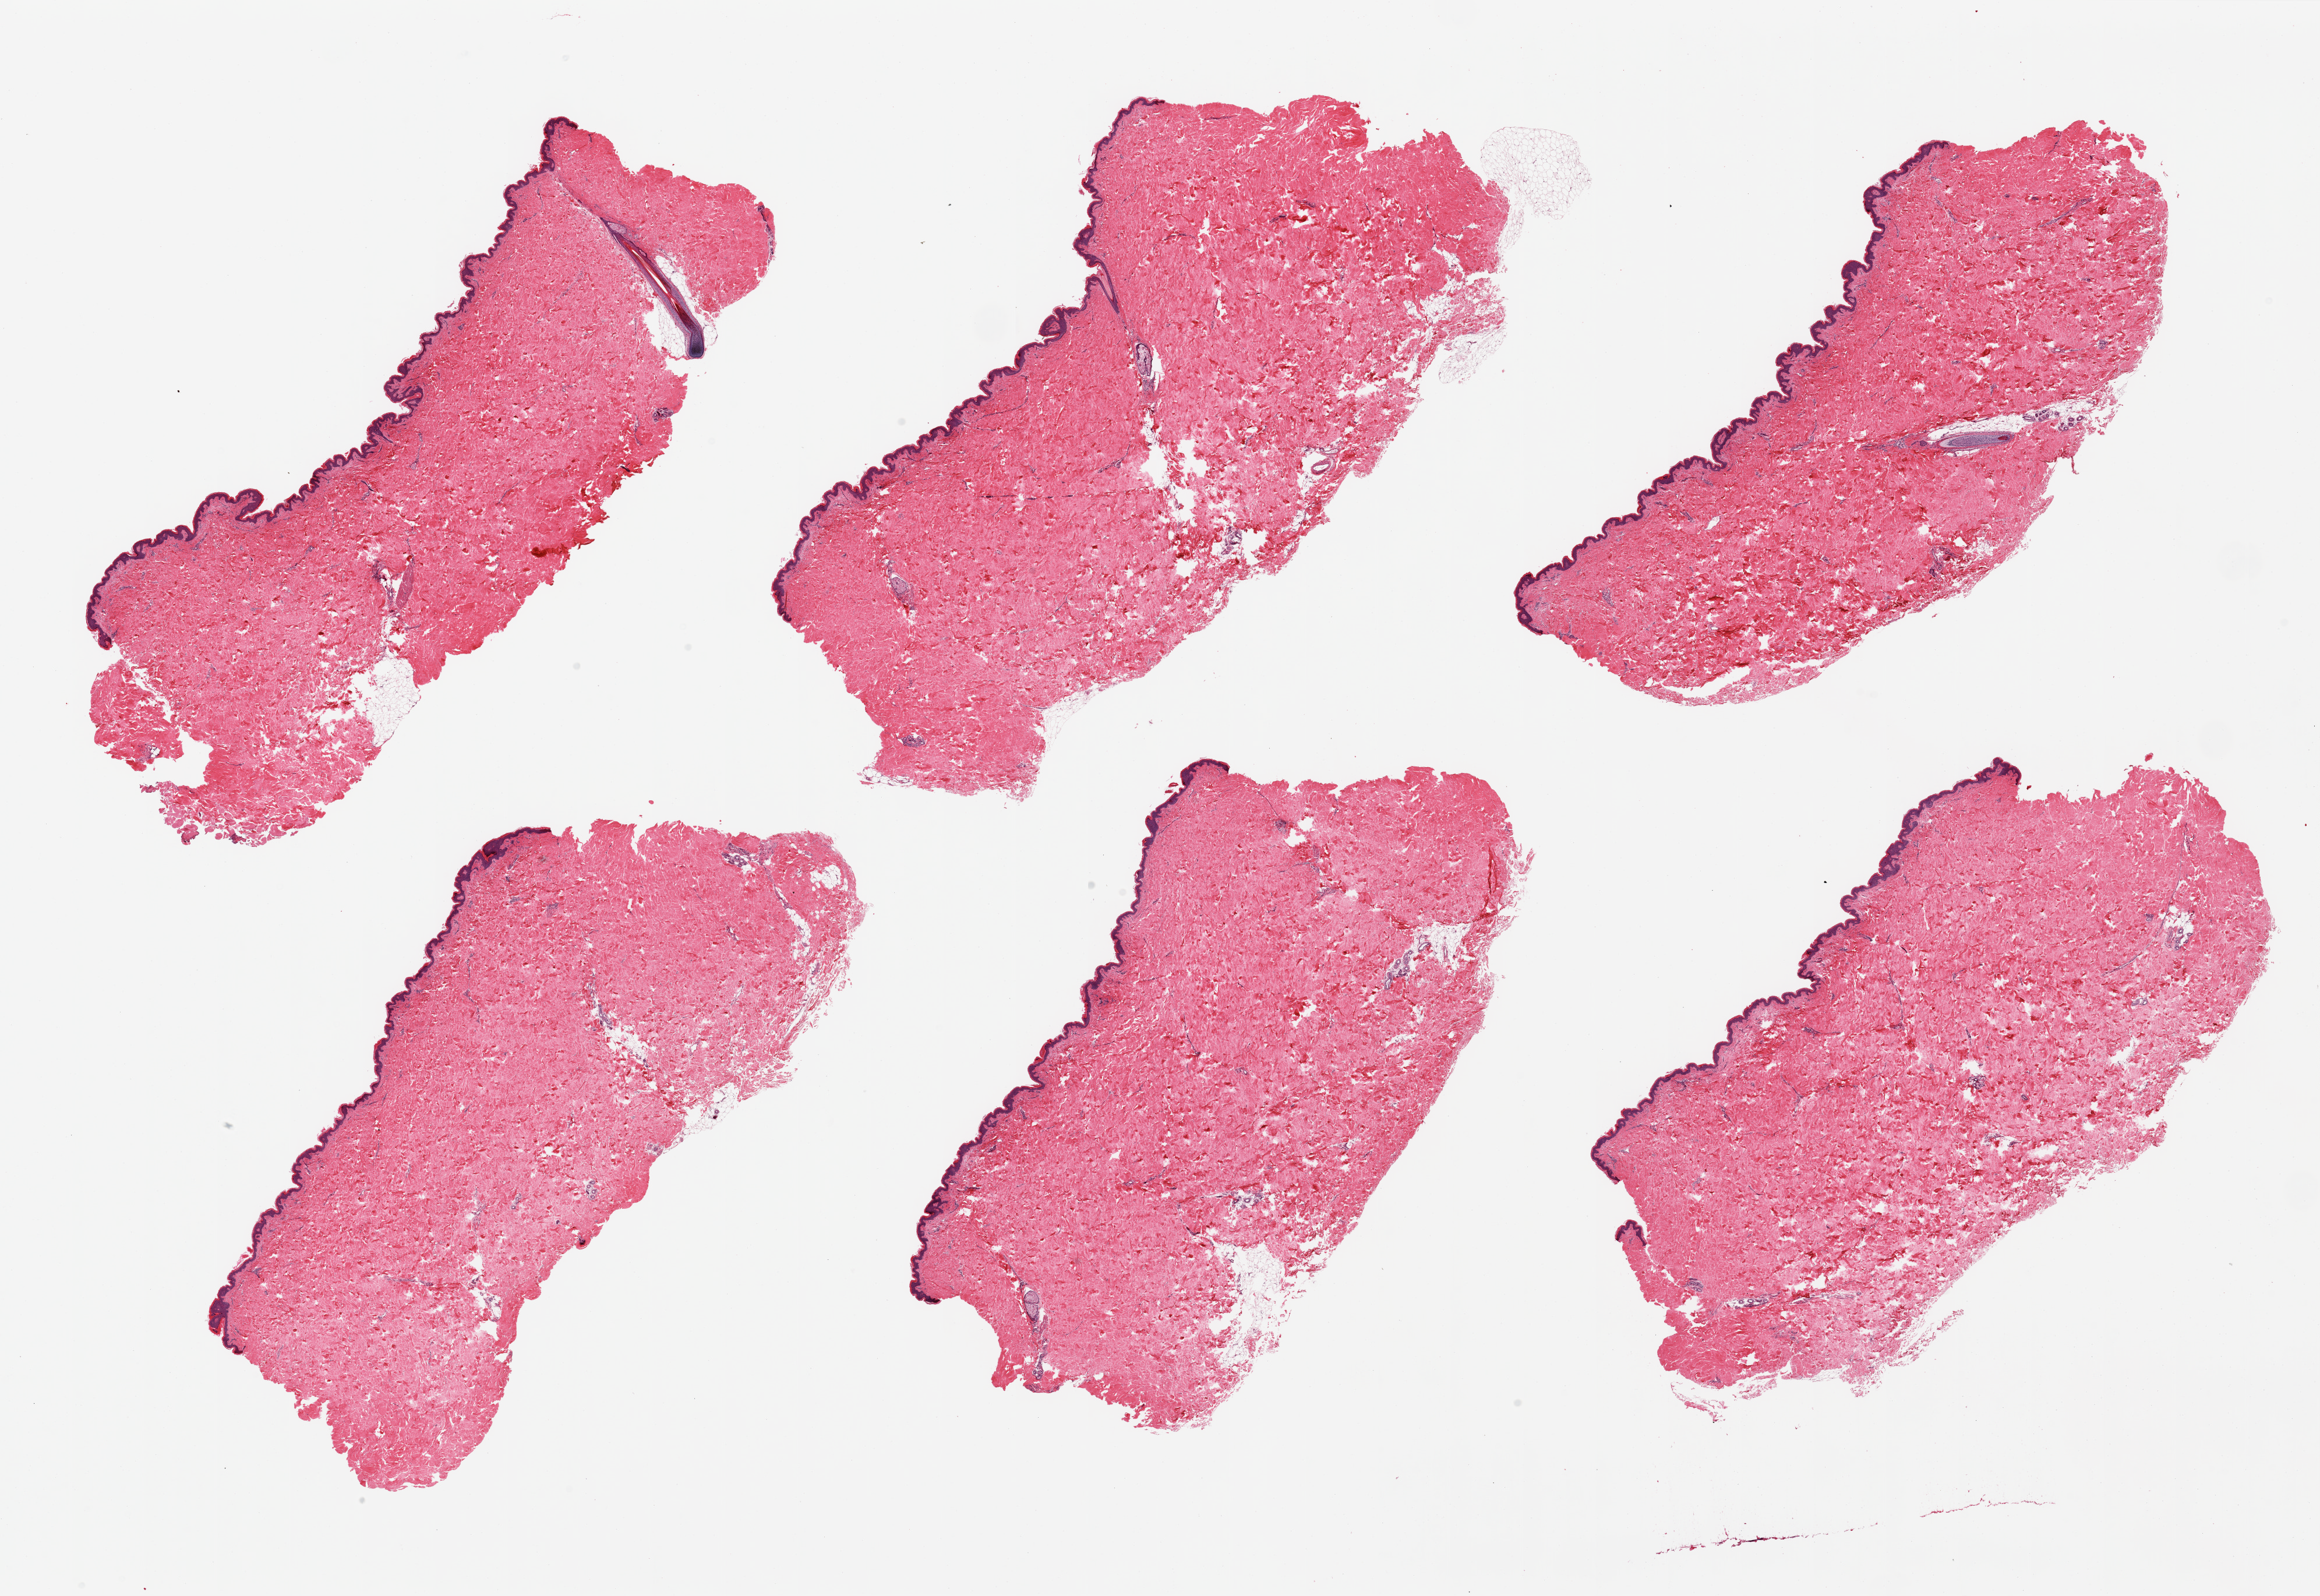
Digitized haematoxylin and eosin-stained section, low-resolution overview of the scanned area, about 31.5 x 21.7 mm. PAXgene-fixed, paraffin-embedded tissue. Sampled site (target tissue): skin of suprapubic region. Tissue donor sample. Donor sex: male.
* reviewer comment on this tissue sample: 6 pieces; well trimmed